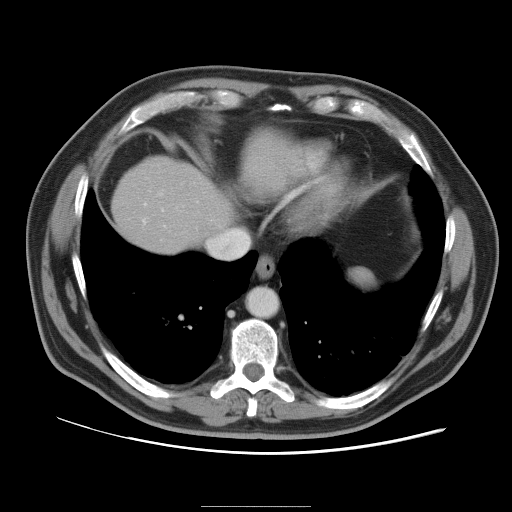
Contrast-enhanced abdominal CT, one axial slice. Slice 90 of 105 in the series (ordered by position). 120 kVp. Intravenous contrast given. Soft-tissue window (W 400 / L 40 HU). 512 × 512 image matrix, field of view 399 × 399 mm. Male patient, age 64 years. From the clinical record (not read from this slice): diagnosis: colorectal cancer liver metastases, imaged before liver resection; multiple liver metastases: yes; largest metastasis: 3 cm.
Annotated regions visible in this slice (expert manual segmentation):
- hepatic veins: box from (x=143, y=220) to (x=146, y=223) px
- liver: (x=114, y=157)–(x=232, y=252)
- planned liver remnant (the part of the liver to remain after resection): (x=114, y=160)–(x=220, y=252)